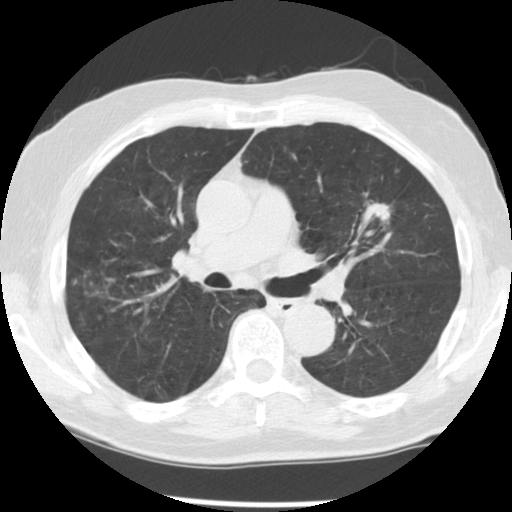
Low-dose screening chest CT, one axial slice; position 76 of 131 along the scan axis; reconstruction kernel STANDARD; 140 kVp; lung window (W 1500 / L -600 HU); 2.5 mm slice thickness; 512 × 512 image matrix, field of view 330 × 330 mm.
Outlined on this slice (manually delineated by an expert):
- lesion 1 (tumor, upper lobe of left lung): bounding box <374,203,390,221> (left, top, right, bottom; pixels)